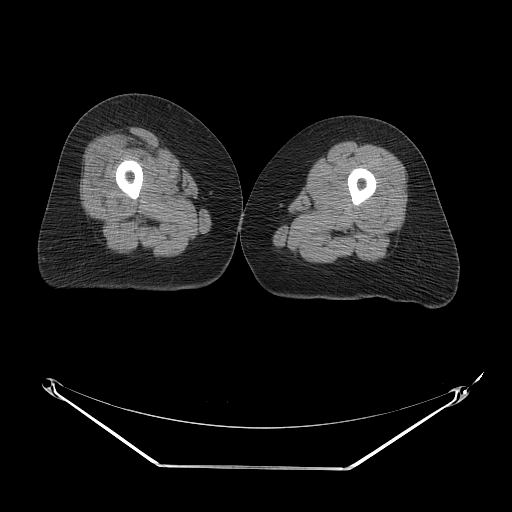
CT of an extremity soft-tissue mass (from a PET/CT study), one axial slice; slice 15 of 267 in the series (ordered by position); reconstruction kernel STANDARD; 140 kVp; soft-tissue window (W 400 / L 40 HU); 512 × 512 image matrix. Female patient. Case-level facts recorded for this patient, not image findings: histological type: malignant solitary fibrous tumor; grade: intermediate; site of the primary tumour: right thigh.
Annotated regions visible in this slice (expert contour drawn on MRI and transferred to this co-registered scan by the dataset authors):
- gross tumour volume including surrounding oedema: bounding box <128,130,181,168> (left, top, right, bottom; pixels)